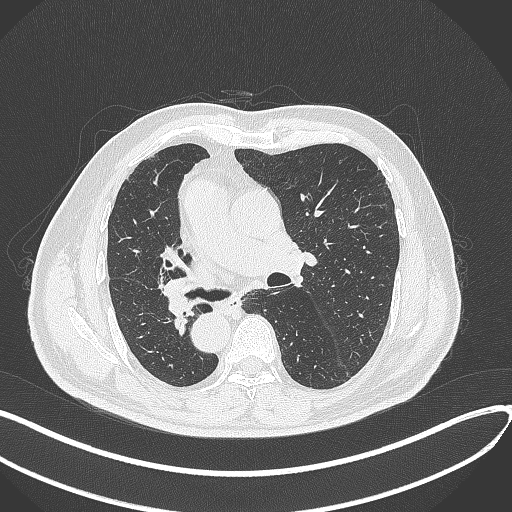
Chest CT, one axial slice; position 160 of 300 along the scan axis; reconstruction kernel B70f; lung window (W 1500 / L -600 HU); 512 × 512 image matrix, field of view 400 × 400 mm. Patient: male, 67 years. From the clinical record (not read from this slice): clinical TNM (as recorded): T2a N0 M0.
Outlined on this slice (bounding box drawn by a radiologist):
- lung tumour (recorded histology: squamous cell carcinoma): bounding box (x1, y1, x2, y2) in pixels: (161, 275, 191, 316)